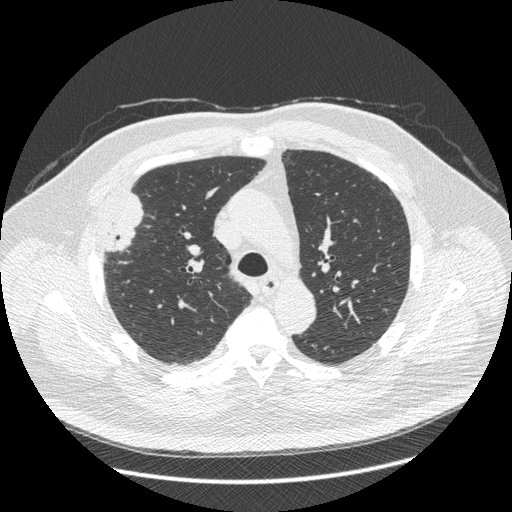
Chest CT (low-dose screening protocol), one axial image, third screening round (two years after baseline), lung window (W 1500 / L -600 HU), 120 kVp, slice 130 of 426 in the series, 512 × 512 image matrix. Male, age 66 years at enrolment. Current smoker at enrolment.
Lesion marked by an expert reader, bounding box (x1, y1, x2, y2) in pixels: (87, 197, 147, 268). The exam's reader record, not a measurement of the box and not confirmed to be the same lesion: non-calcified nodule or mass ≥4 mm, right upper lobe, 48 × 25 mm, spiculated (stellate) margins, soft tissue attenuation, pre-existing on the prior screen: no. Later outcome: lung cancer diagnosed 35 days after this screen — non-small cell carcinoma, right upper lobe, stage IV (AJCC 6th edition), 50 mm at pathology.